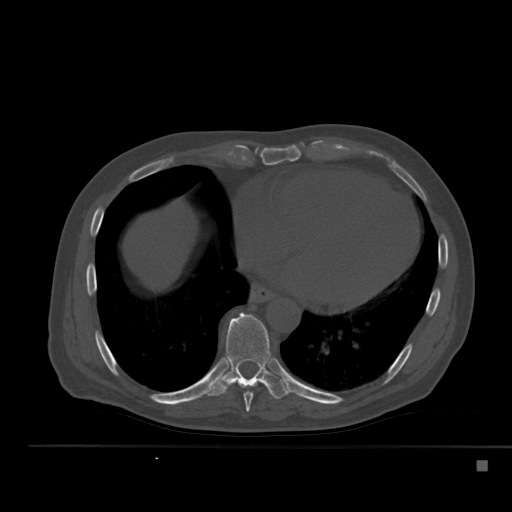
CT including the spine, one axial slice. Position 294 of 517 along the scan axis. Reconstruction kernel Br40s. 120 kVp. Bone window (W 1800 / L 400 HU). 1.5 mm slice thickness. 512 × 512 image matrix, field of view 408 × 408 mm. Patient: male, 70 years. Case-level facts recorded for this patient, not image findings: primary cancer: renal; vertebrae with lytic lesions (as recorded): T4, T6, T10, T12, L3, L4, L5.
Structures marked on this image (semi-automatic segmentation, software-assisted and operator-edited):
- T8 vertebra: bounding box <243,381,260,412> (left, top, right, bottom; pixels)
- T9 vertebra: <208,312,287,400>